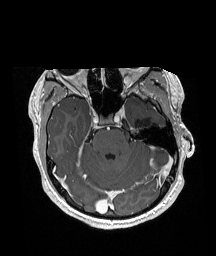
Brain MRI from a brain-tumour surgery series, one axial slice. Position 122 of 192 along the scan axis. T1-weighted post-contrast. 216 × 256 image matrix, field of view 211 × 250 mm. Case-level facts recorded for this patient, not image findings: histopathology: Glioneuronal tumor; WHO grade: 2; tumour location: Left Superior Temporal Gyrus.
Outlined on this slice (expert manual segmentation):
- previous resection cavity: box from (x=135, y=118) to (x=151, y=131) px